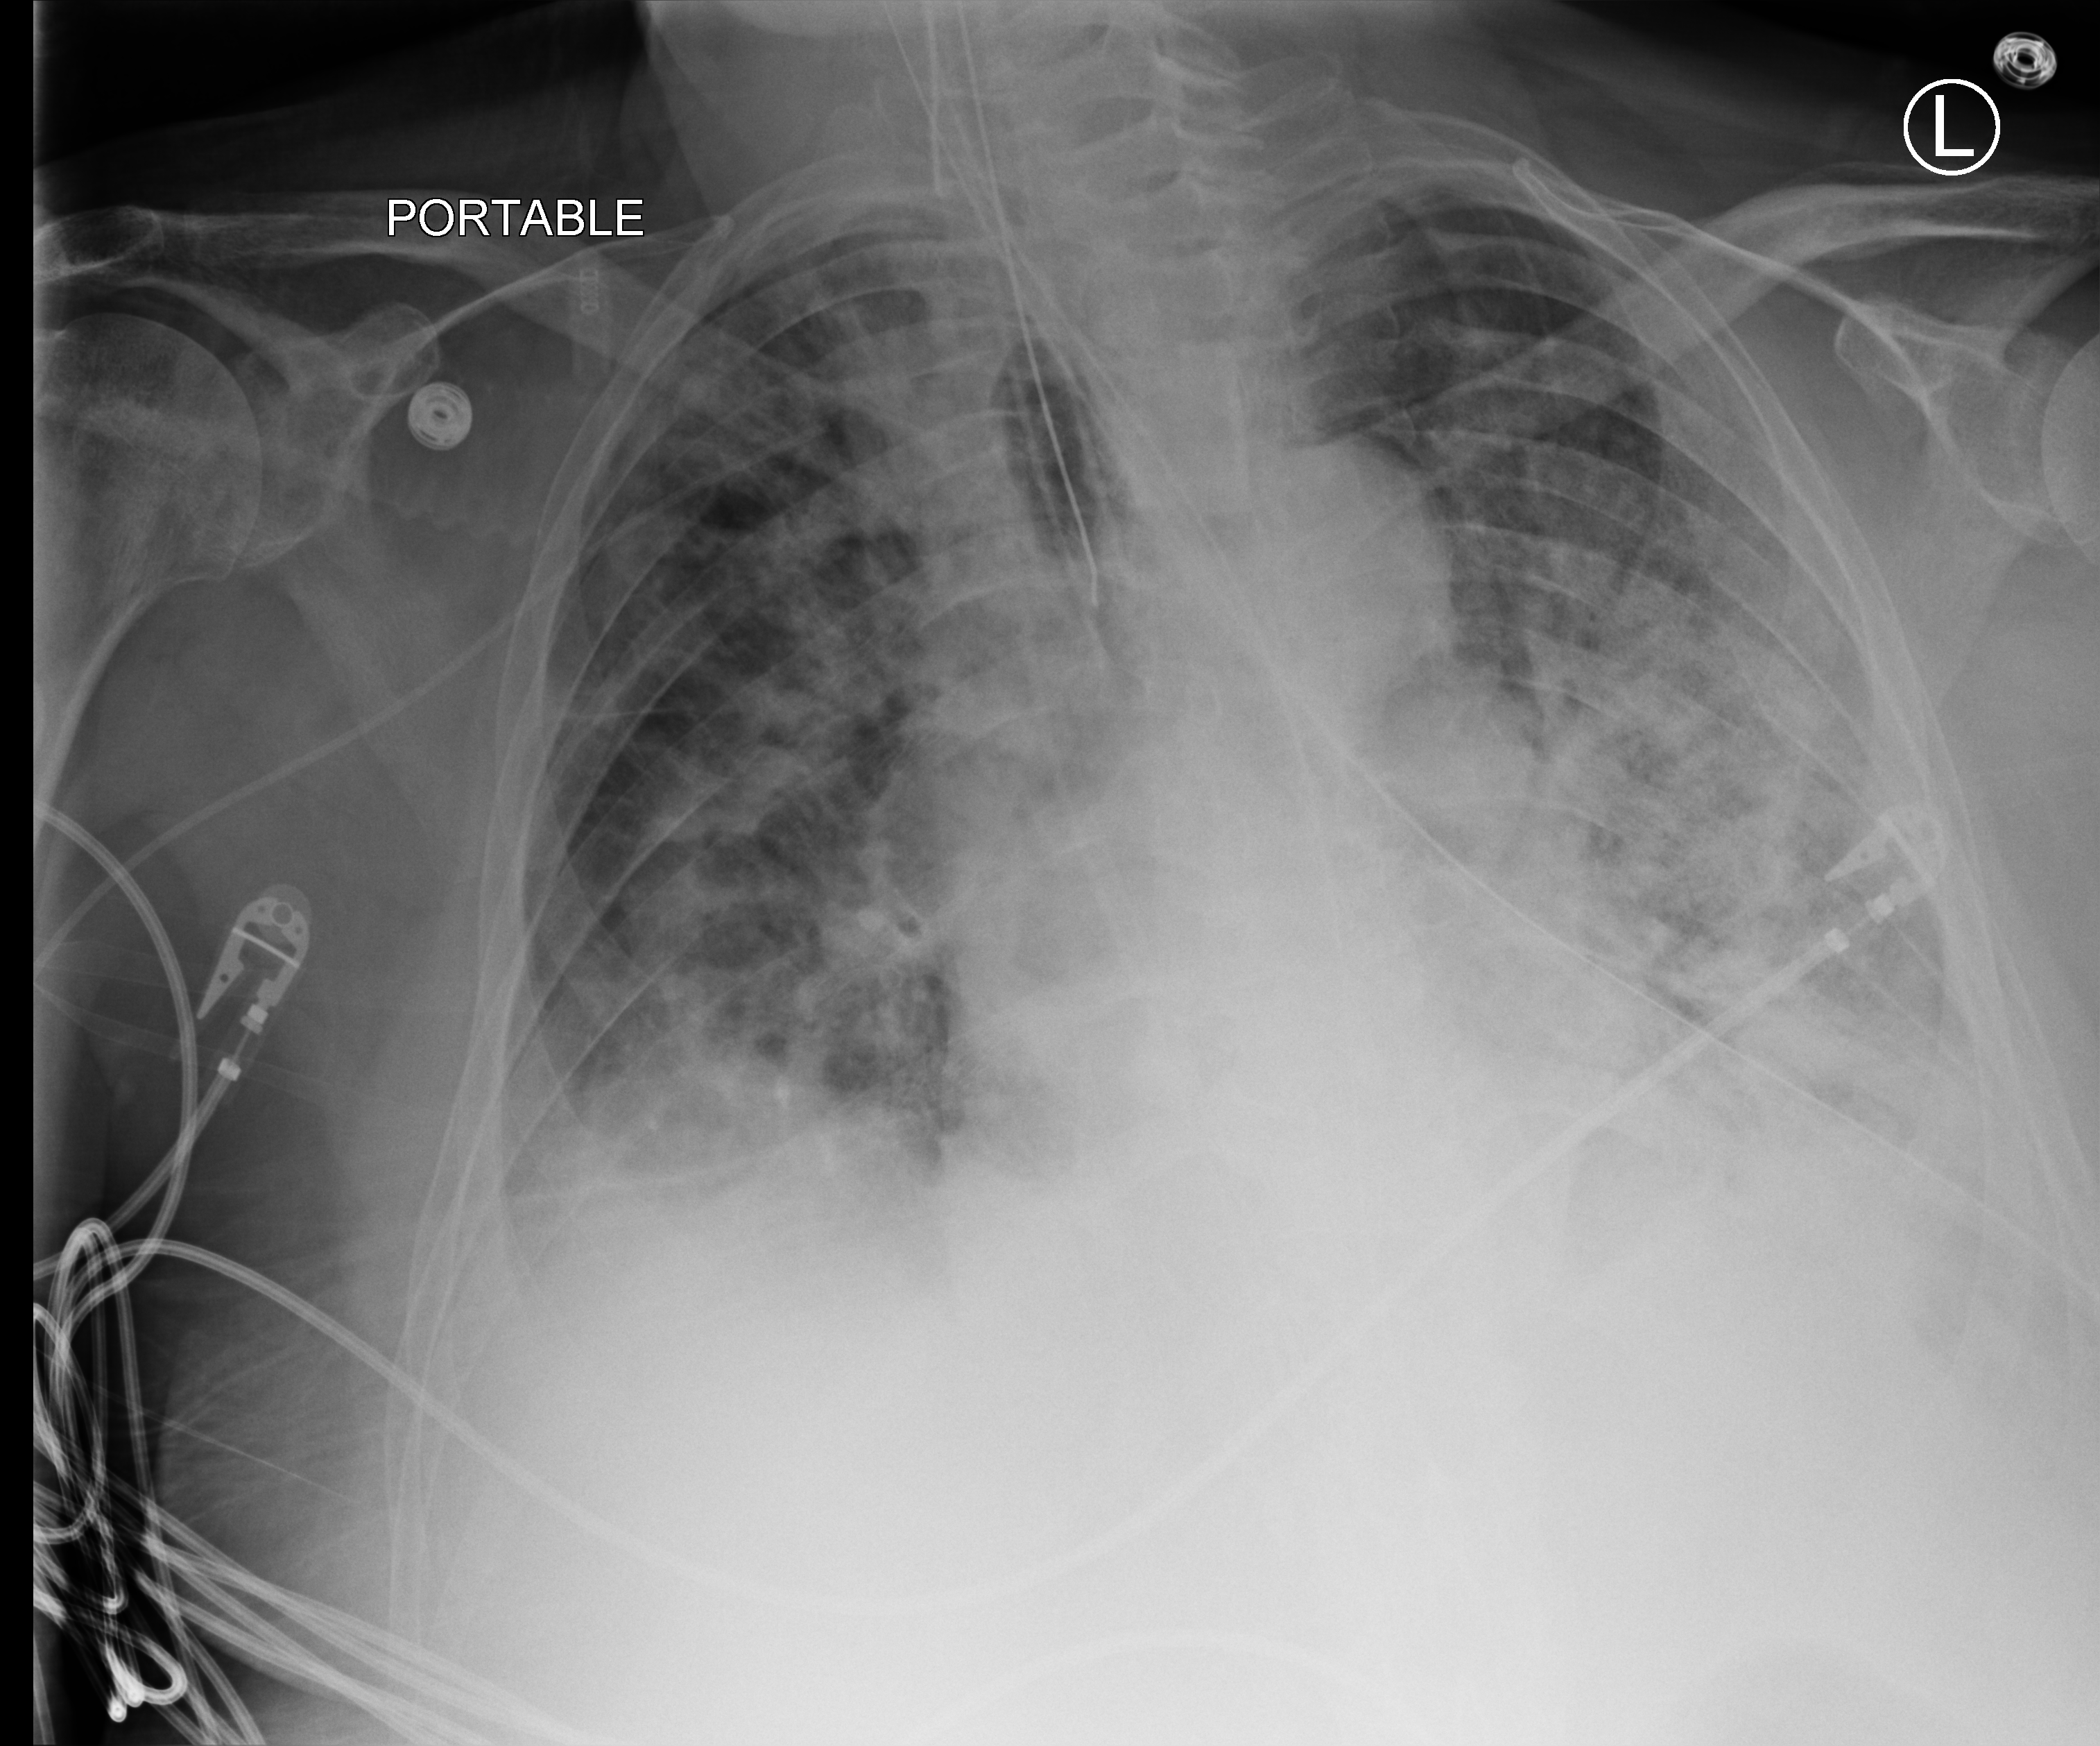
Bedside chest radiograph (computed radiography), anteroposterior (AP) projection. Male patient hospitalised with COVID-19, age 60–74 years.
Admission-level facts for this patient (not findings on this image; timing relative to this image not recorded):
- other chronic lung disease (admission record): no
- admitted to intensive care during this hospital stay: yes
- mechanically ventilated during this hospital stay: yes